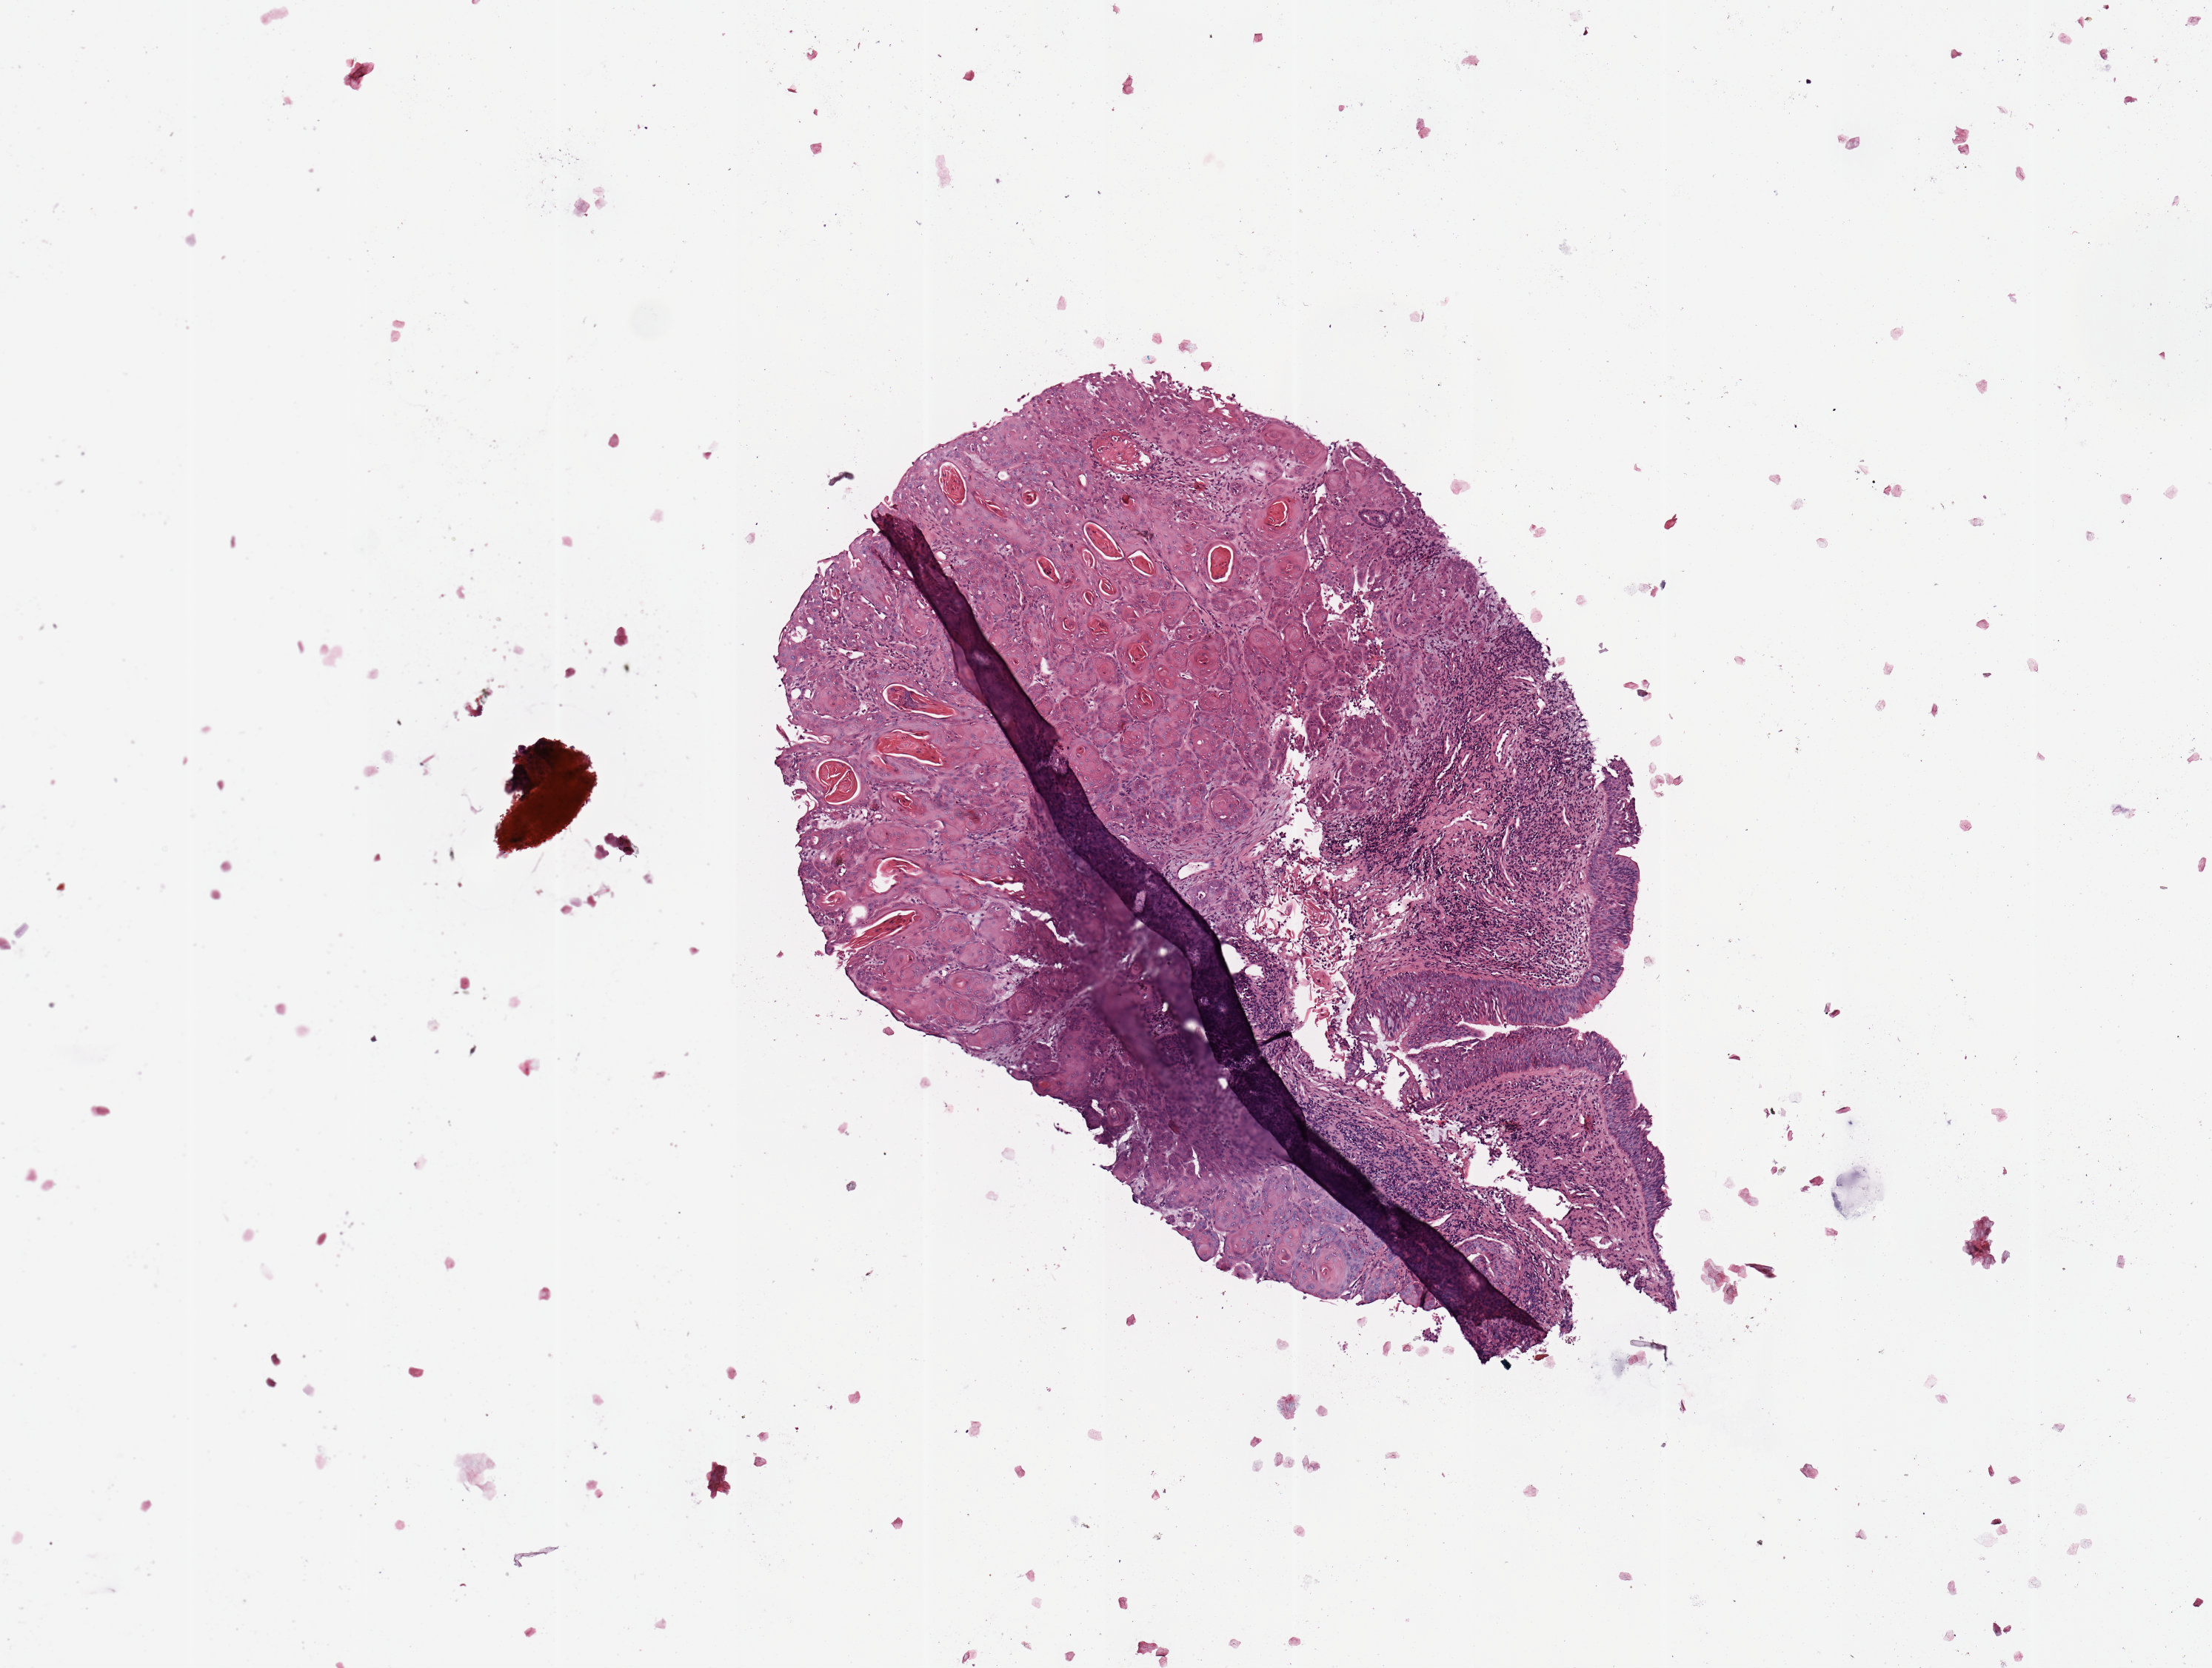
H&E-stained whole-slide image, whole scanned area (about 5.9 x 4.5 mm, from a 20x scan) shown as a low-resolution overview. Head and neck, tissue type not recorded. Patient: male, age 52 years.
Patient diagnosis: Squamous cell carcinoma, NOS (larynx, NOS).